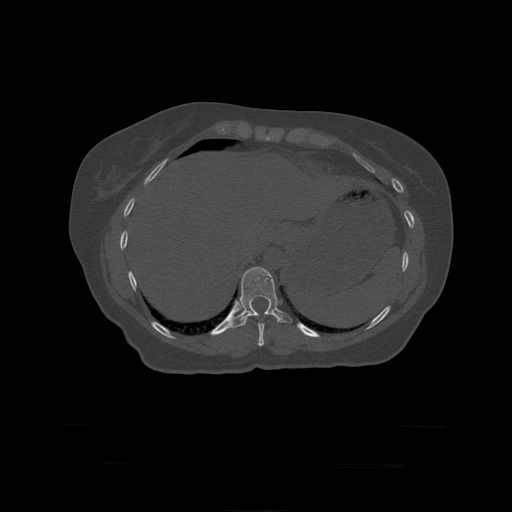
CT including the spine, one axial slice. Position 227 of 399 along the scan axis. Bone window (W 1800 / L 400 HU). 512 × 512 image matrix, field of view 450 × 450 mm. Patient age 41 years. From the clinical record (not read from this slice): primary cancer: breast.
Structures marked on this image (semi-automatic segmentation, software-assisted and operator-edited):
- T10 vertebra: bounding box (x1, y1, x2, y2) in pixels: (258, 323, 265, 346)
- T11 vertebra: (227, 267, 292, 330)